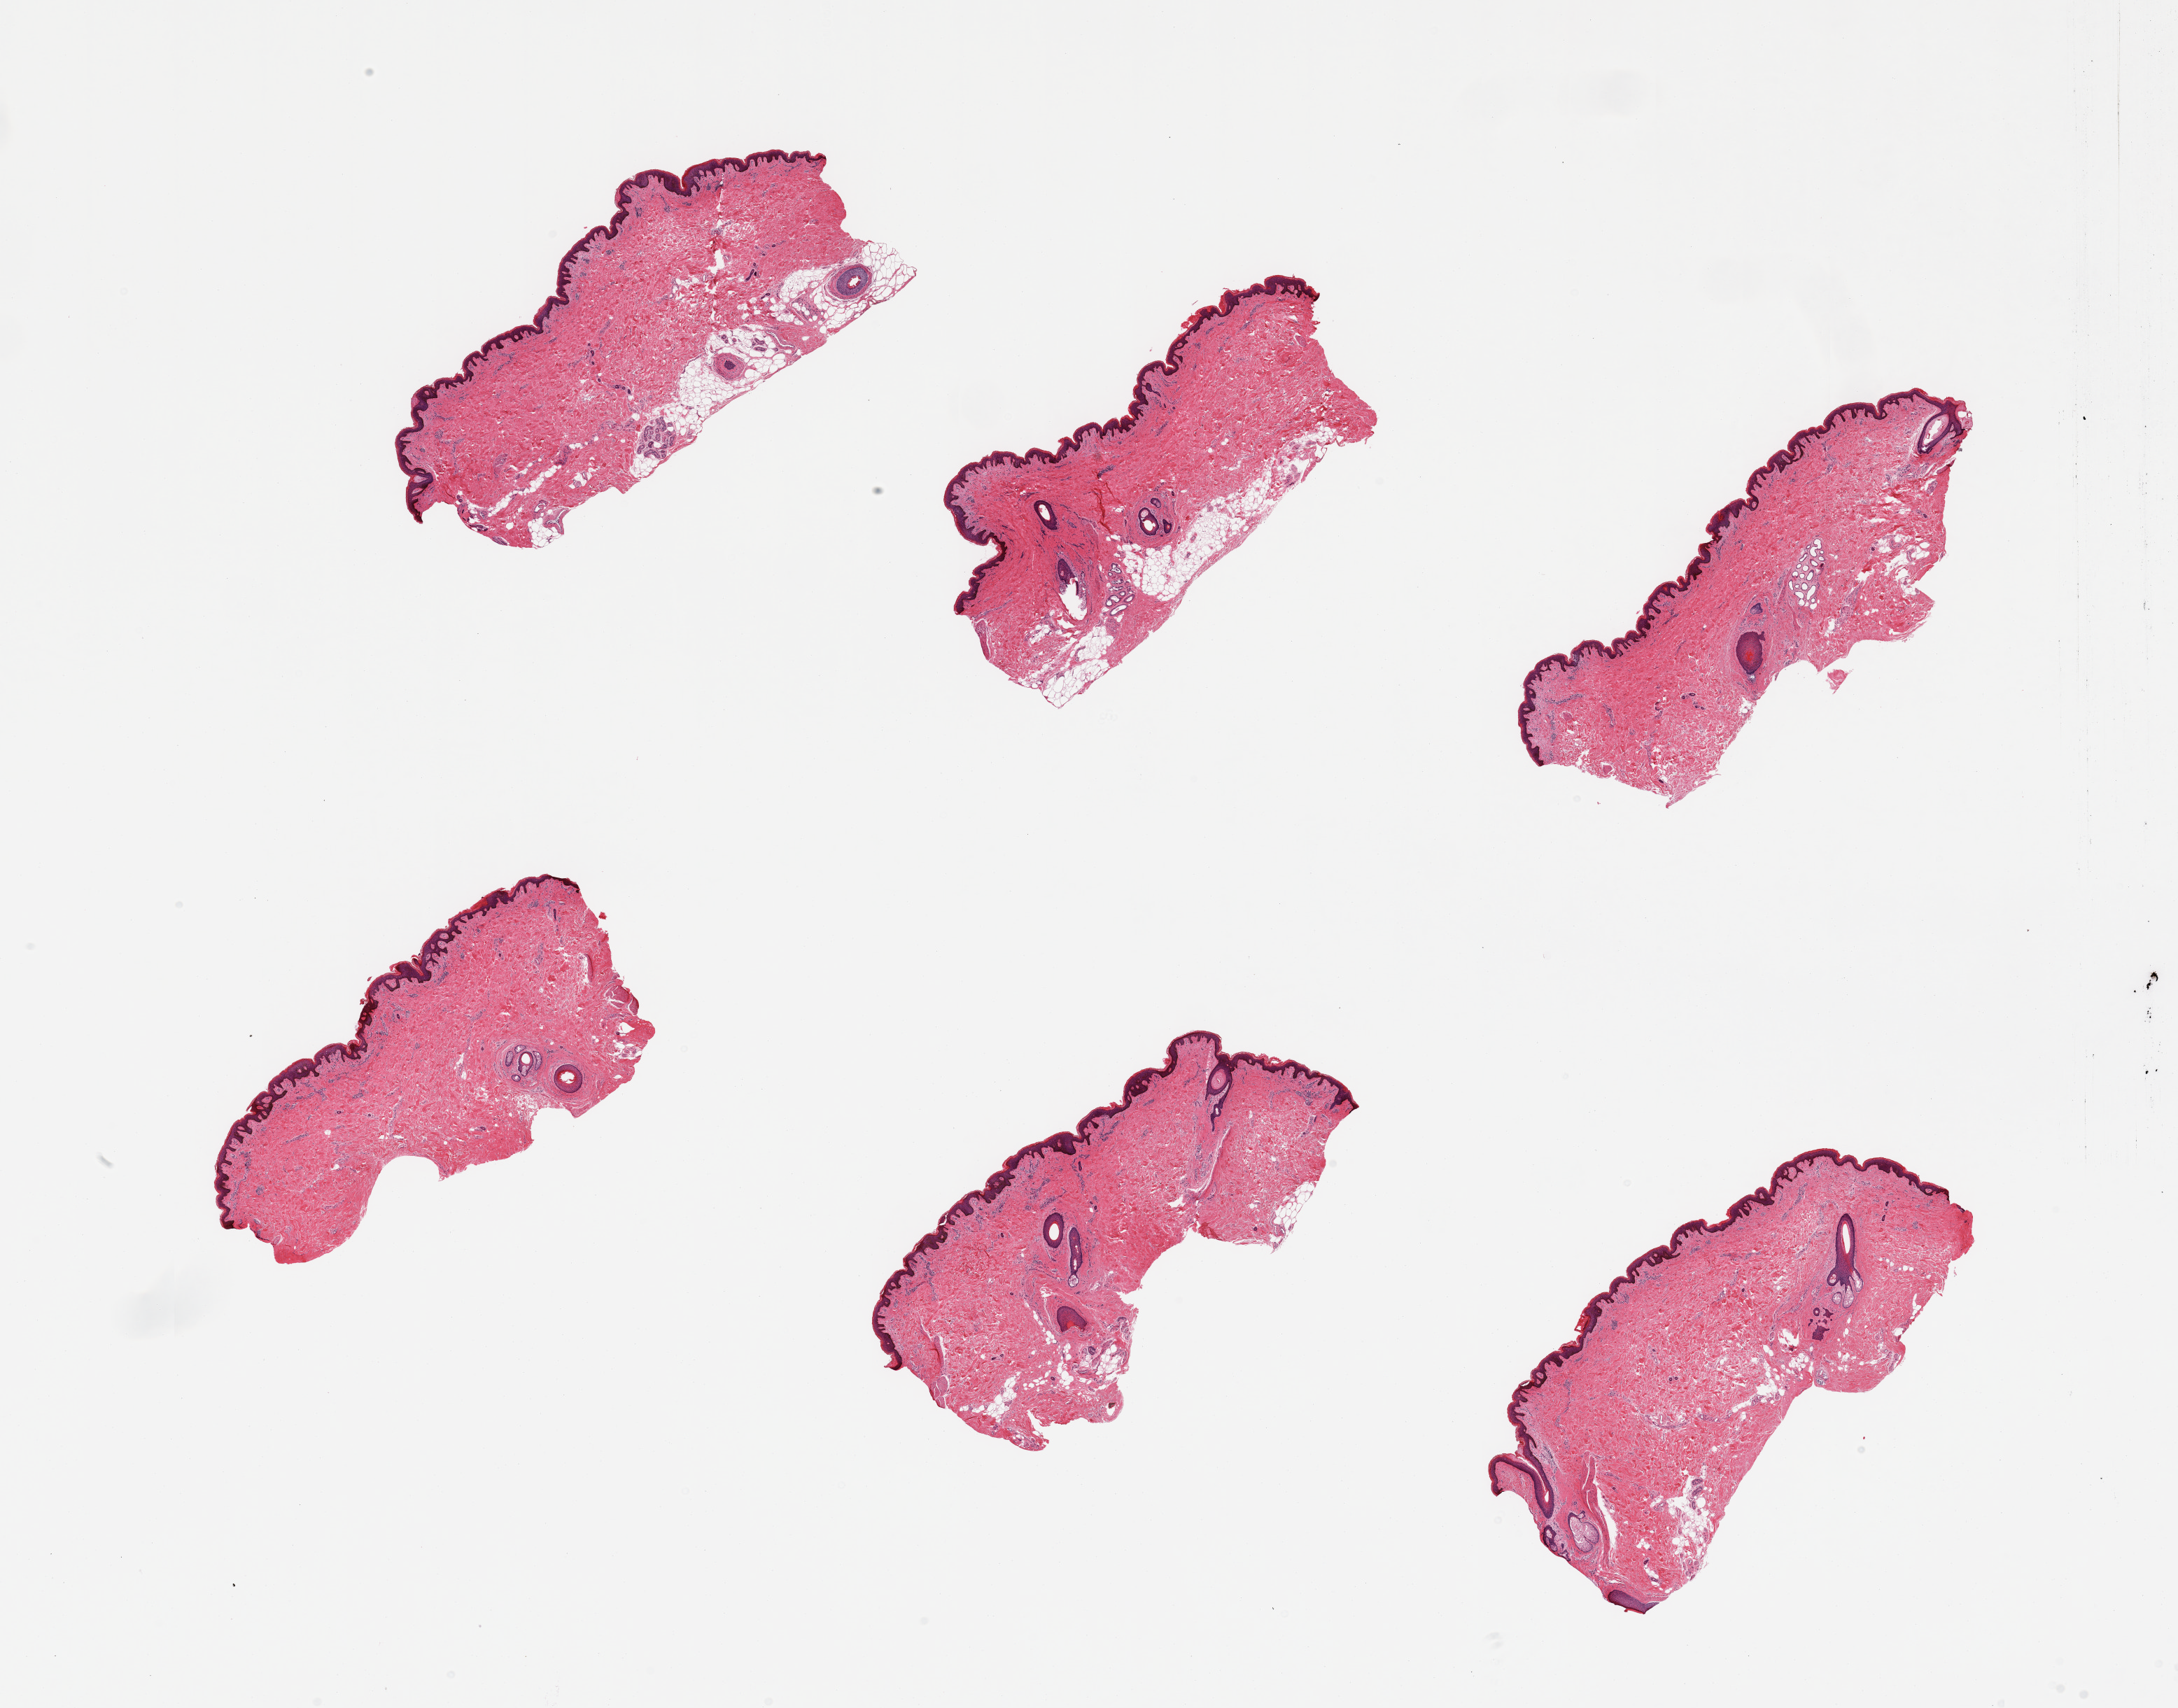
Hematoxylin and eosin (H&E) whole-slide image, brightfield — low-resolution overview of the scanned area, about 24.6 x 19.3 mm, PAXgene-fixed paraffin-embedded (PFPE) section, target tissue: skin of suprapubic region, donor tissue sample. Donor sex: male.
Reviewer comment on this tissue sample: 6 pieces; 2 have 20% dermal fat.